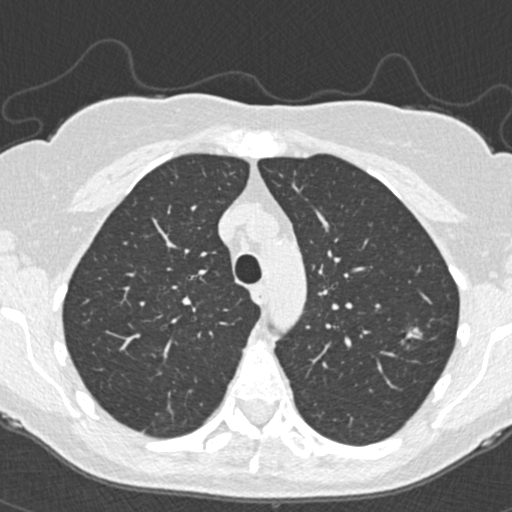
Low-dose screening chest CT, one axial slice. Slice 268 of 350 in the series (ordered by position). 120 kVp. Lung window (W 1500 / L -600 HU). 1 mm slice thickness. 512 × 512 image matrix.
Structures marked on this image (expert manual segmentation):
- lesion 1 (tumor, upper lobe of left lung): bounding box <406,327,422,339> (left, top, right, bottom; pixels)